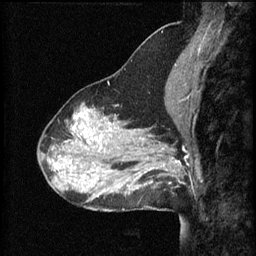
Breast MRI (dynamic contrast-enhanced), one sagittal slice; position 23 of 60 along the scan axis; 3 images stored at this slice position (order not interpretable as contrast timing); 1.5 T; TE 4.2 ms, TR 8.2 ms; 2 mm slice thickness; 256 × 256 image matrix. Female patient, age 37 years.
Outlined on this slice (semi-automatically segmented with operator editing):
- analysis volume of interest (the breast-tissue region the enhancement analysis was run in; not a lesion): bounding box <148,140,193,185> (left, top, right, bottom; pixels)
- tumour enhancement mask (voxels above the 70 % enhancement threshold inside the analysis volume of interest): <148,160,179,185>